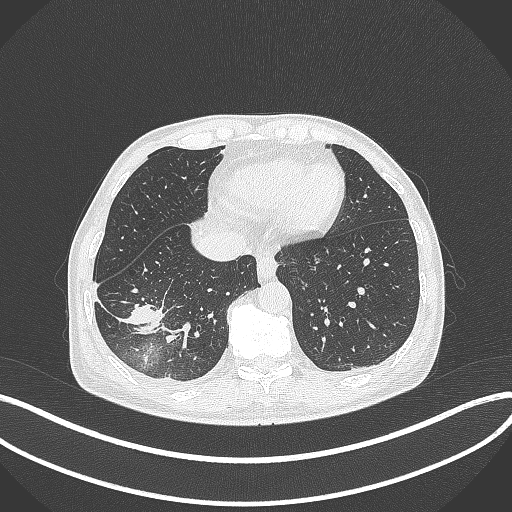
Chest CT, one axial slice; reconstruction kernel B70f; 120 kVp; lung window (W 1500 / L -600 HU); 1 mm slice thickness; 512 × 512 image matrix, field of view 400 × 400 mm. Male patient, age 64 years. From the clinical record (not read from this slice): clinical TNM (as recorded): T3 N0 M0; histopathological grade: G2-3.
Structures marked on this image (rectangle marked by the reading radiologist):
- lung tumour (recorded histology: adenocarcinoma): box from (x=116, y=298) to (x=165, y=340) px